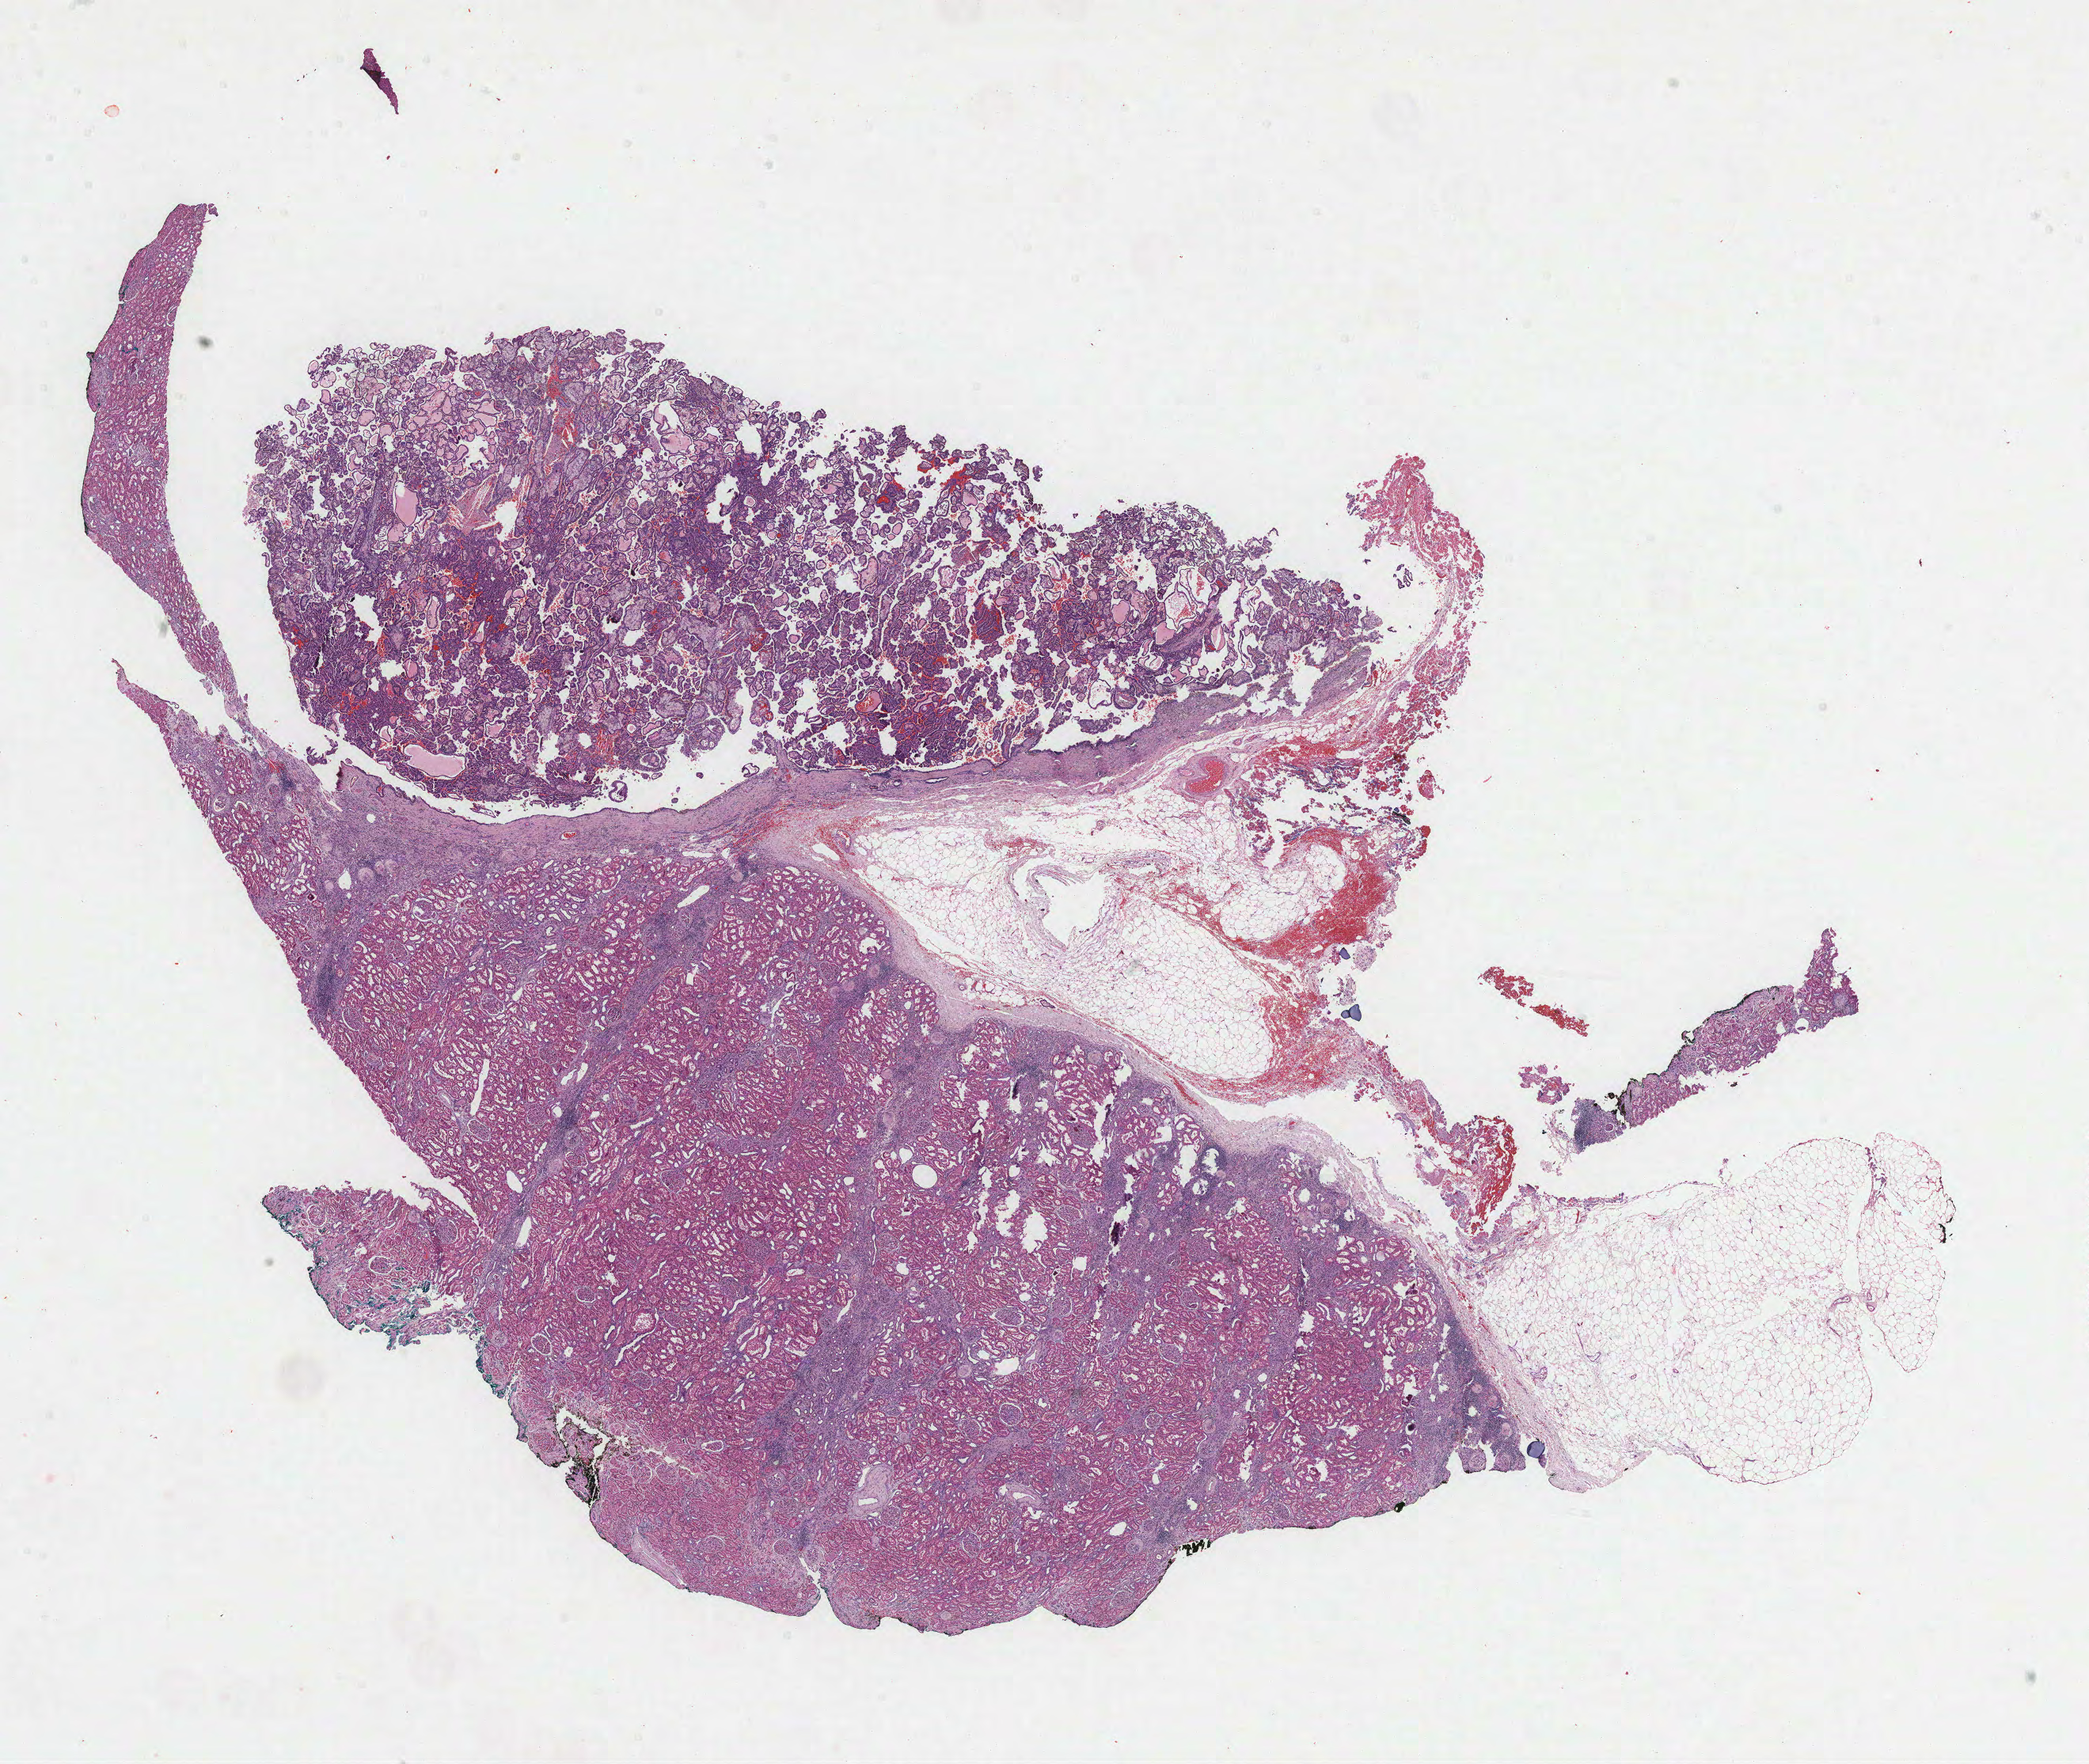
H&E-stained whole-slide image — low-resolution overview of the scanned area, about 21.3 x 18.0 mm, formalin-fixed paraffin-embedded (FFPE) diagnostic section, sample: primary tumour, kidney. Male, age 60 years at initial diagnosis.
* histologic diagnosis: Papillary adenocarcinoma, NOS
* TNM: T1a NX MX
* laterality: left
* AJCC pathologic stage: I (6th edition)